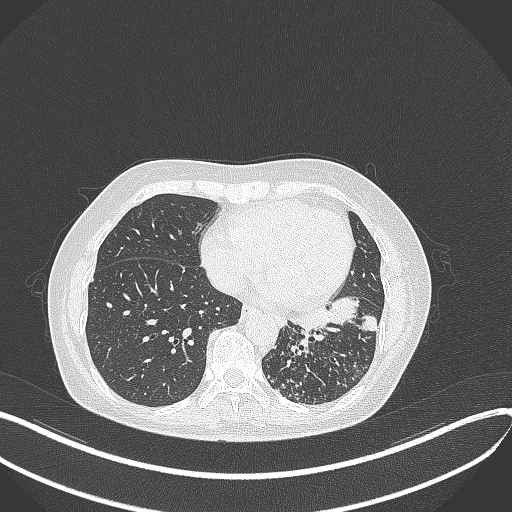
Chest CT, one axial slice; position 142 of 429 along the scan axis; reconstruction kernel B70f; lung window (W 1500 / L -600 HU); 1 mm slice thickness; 512 × 512 image matrix, field of view 400 × 400 mm. Female patient, age 63 years. Case-level facts recorded for this patient, not image findings: clinical TNM (as recorded): T1b N0 M0; histopathological grade: G2-3.
Structures marked on this image (rectangle marked by the reading radiologist):
- lung tumour (recorded histology: adenocarcinoma): bounding box (x1, y1, x2, y2) in pixels: (285, 294, 377, 341)